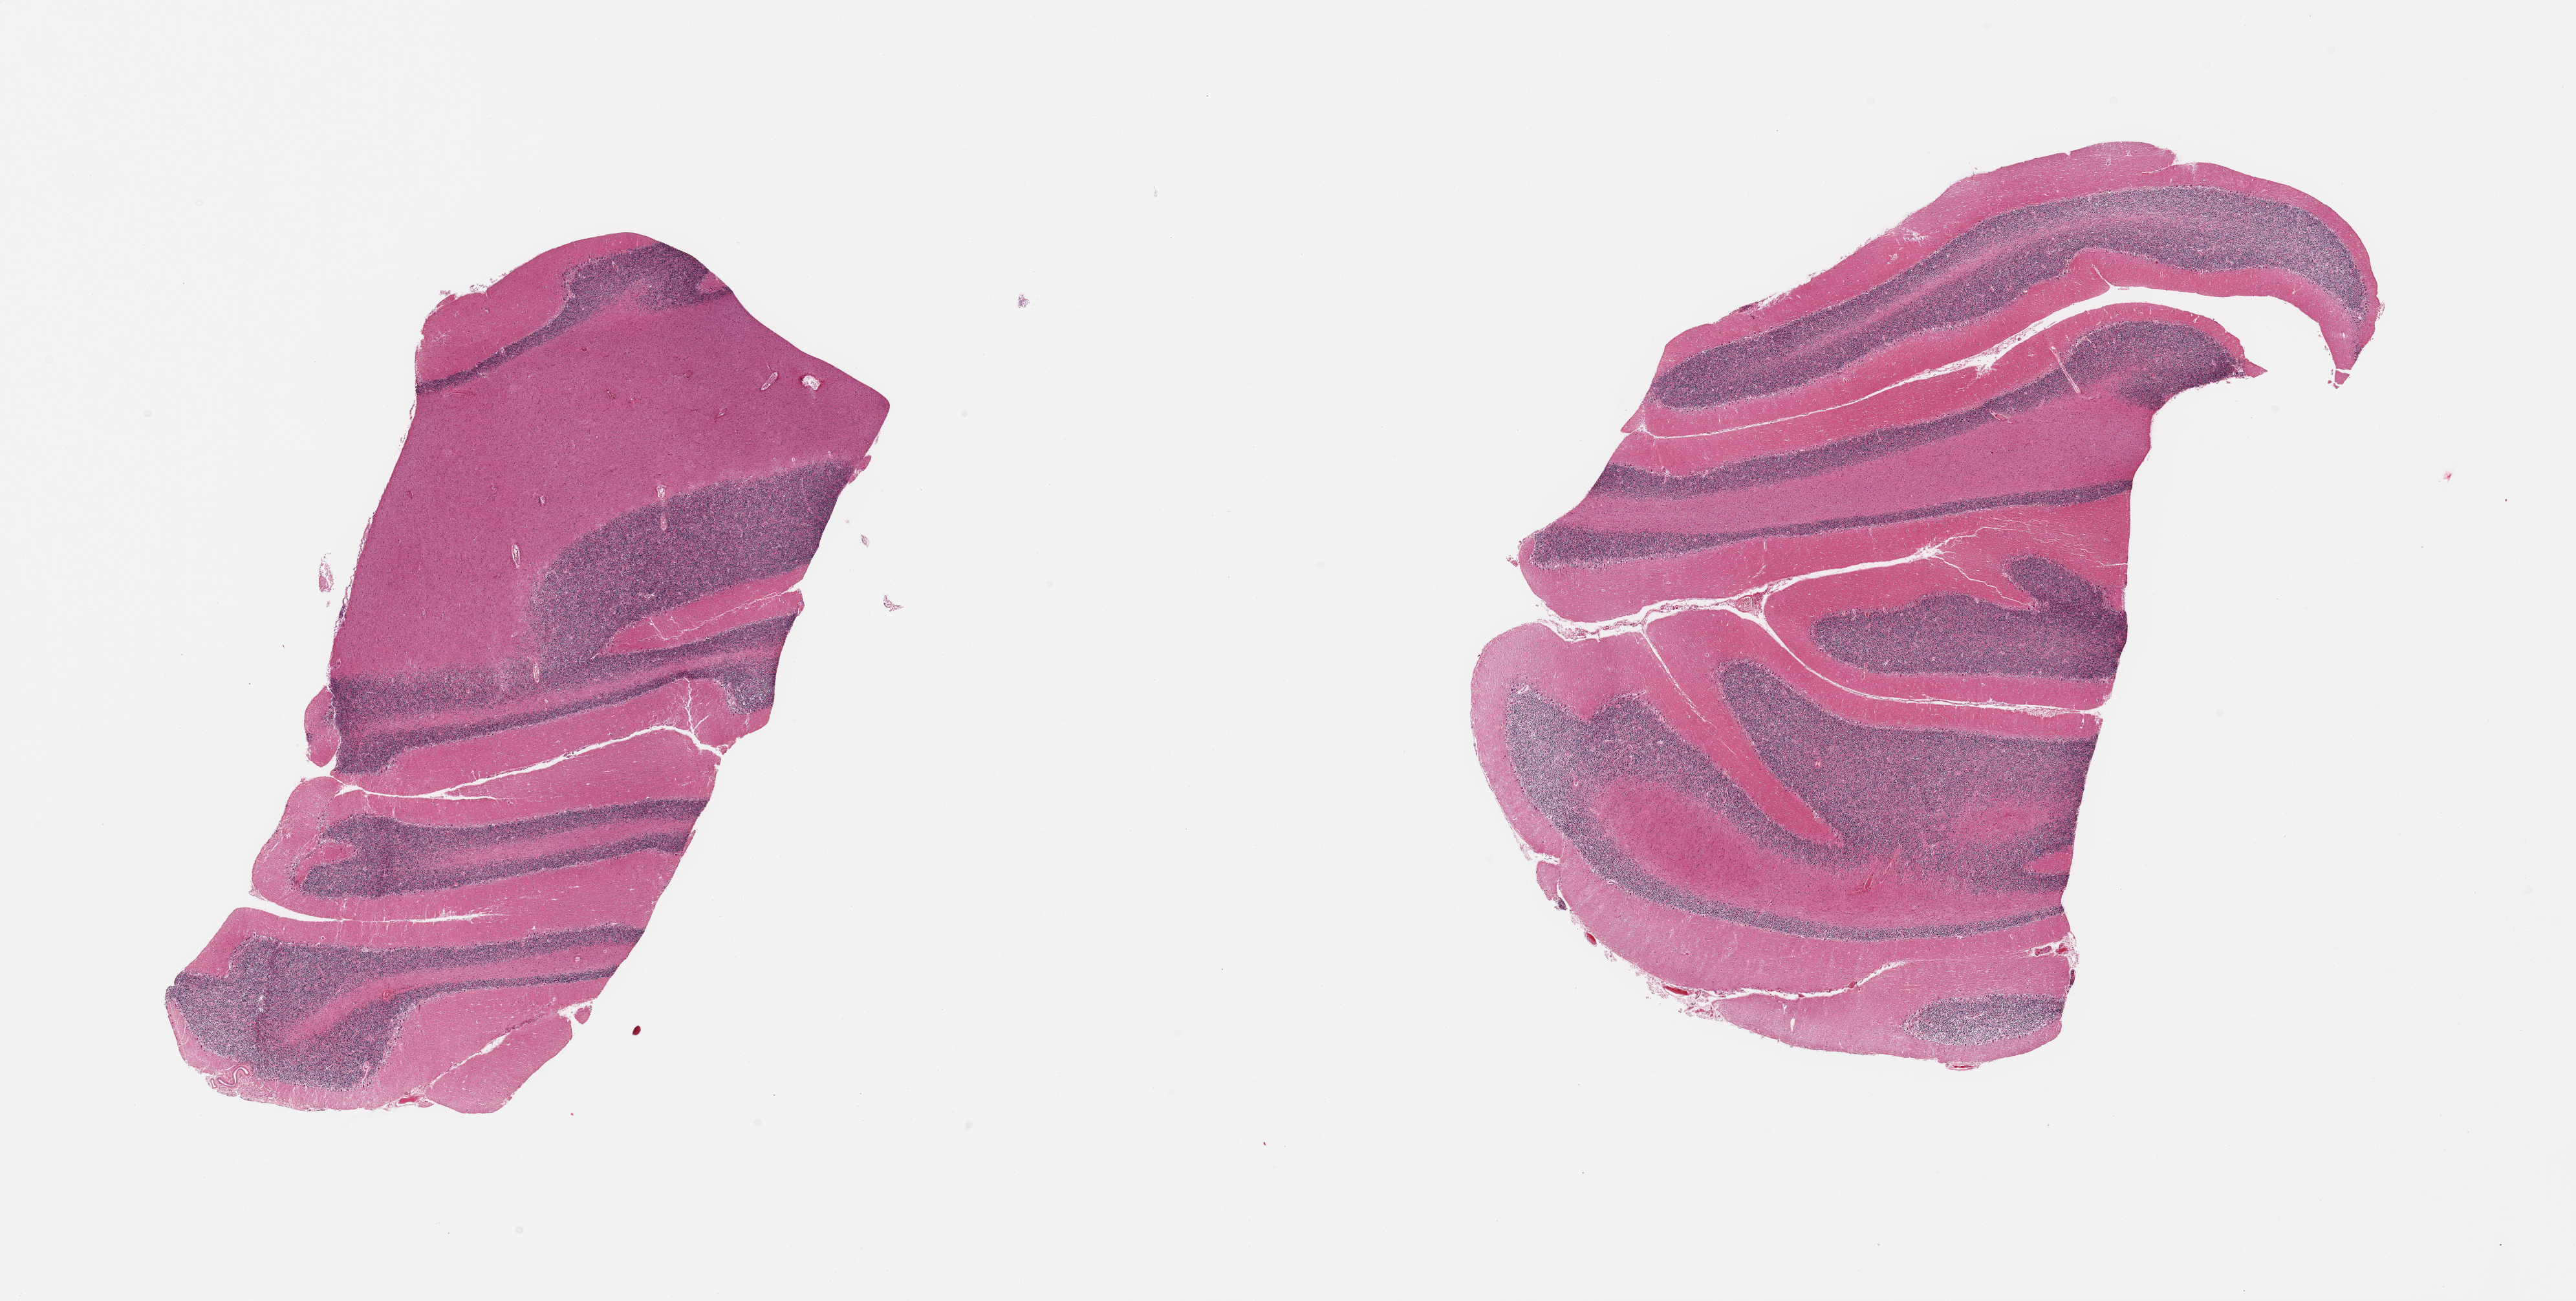
Whole-slide image, H&E stain, brightfield, low-resolution overview of the scanned area, about 31.5 x 15.9 mm. PAXgene-fixed, paraffin-embedded tissue. Sampled site (target tissue): cerebellum. Tissue donor sample.
Pathologist's review note for this sample: 2 pieces; no abnormalities.